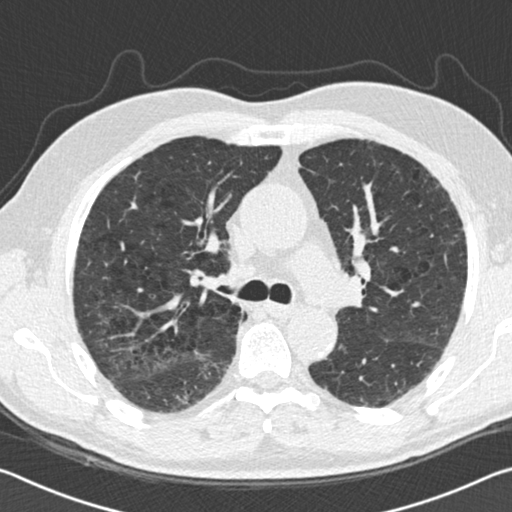
Axial slice from a low-dose chest CT screening exam. Second annual screen. Lung window (W 1500 / L -600 HU). Standard (soft-tissue) reconstruction kernel (B30f). Male, age 69 years at enrolment. Current smoker at enrolment.
• Lesion marked by an expert reader, bounding box (x1, y1, x2, y2) in pixels: (160, 376, 210, 424).
• Reader record for this screening exam (exam-level; its link to the box is not recorded): non-calcified nodule or mass ≥4 mm, right lower lobe, 10 × 10 mm, spiculated (stellate) margins, soft tissue attenuation, pre-existing on the prior screen: yes; interval growth: yes.